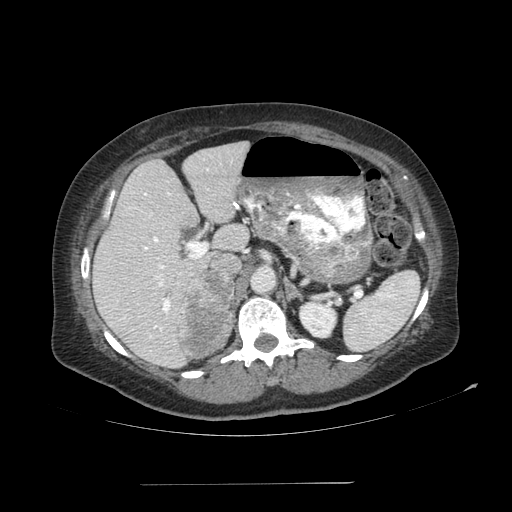
Contrast-enhanced abdominal CT, one axial slice. 120 kVp. Soft-tissue window (W 400 / L 40 HU). 2.5 mm slice thickness. 512 × 512 image matrix, field of view 440 × 440 mm. Patient: female, 67 years. Case-level facts recorded for this patient, not image findings: diagnosis: adrenocortical carcinoma; tumour side: right adrenal; tumour size at pathology: 9.8 cm; Ki-67 index: 59 %; stage (as recorded): 4.
Outlined on this slice (semi-automatic segmentation, software-assisted and operator-edited):
- mass: box from (x=177, y=271) to (x=233, y=357) px